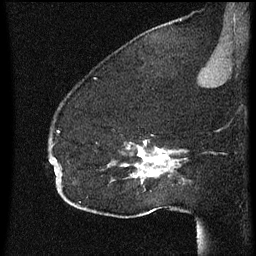
Breast MRI (dynamic contrast-enhanced), one sagittal slice; position 47 of 60 along the scan axis; dynamic contrast-enhanced series, image 2 of 3 at this slice position (ordered by acquisition); 1.5 T; TE 4.2 ms, TR 8 ms; 2 mm slice thickness; 256 × 256 image matrix, field of view 180 × 180 mm. Patient: female, 52 years.
Annotated regions visible in this slice (semi-automatic segmentation, software-assisted and operator-edited):
- analysis volume of interest (the breast-tissue region the enhancement analysis was run in; not a lesion): bounding box <54,112,178,207> (left, top, right, bottom; pixels)
- tumour enhancement mask (voxels above the 70 % enhancement threshold inside the analysis volume of interest): <55,132,173,181>